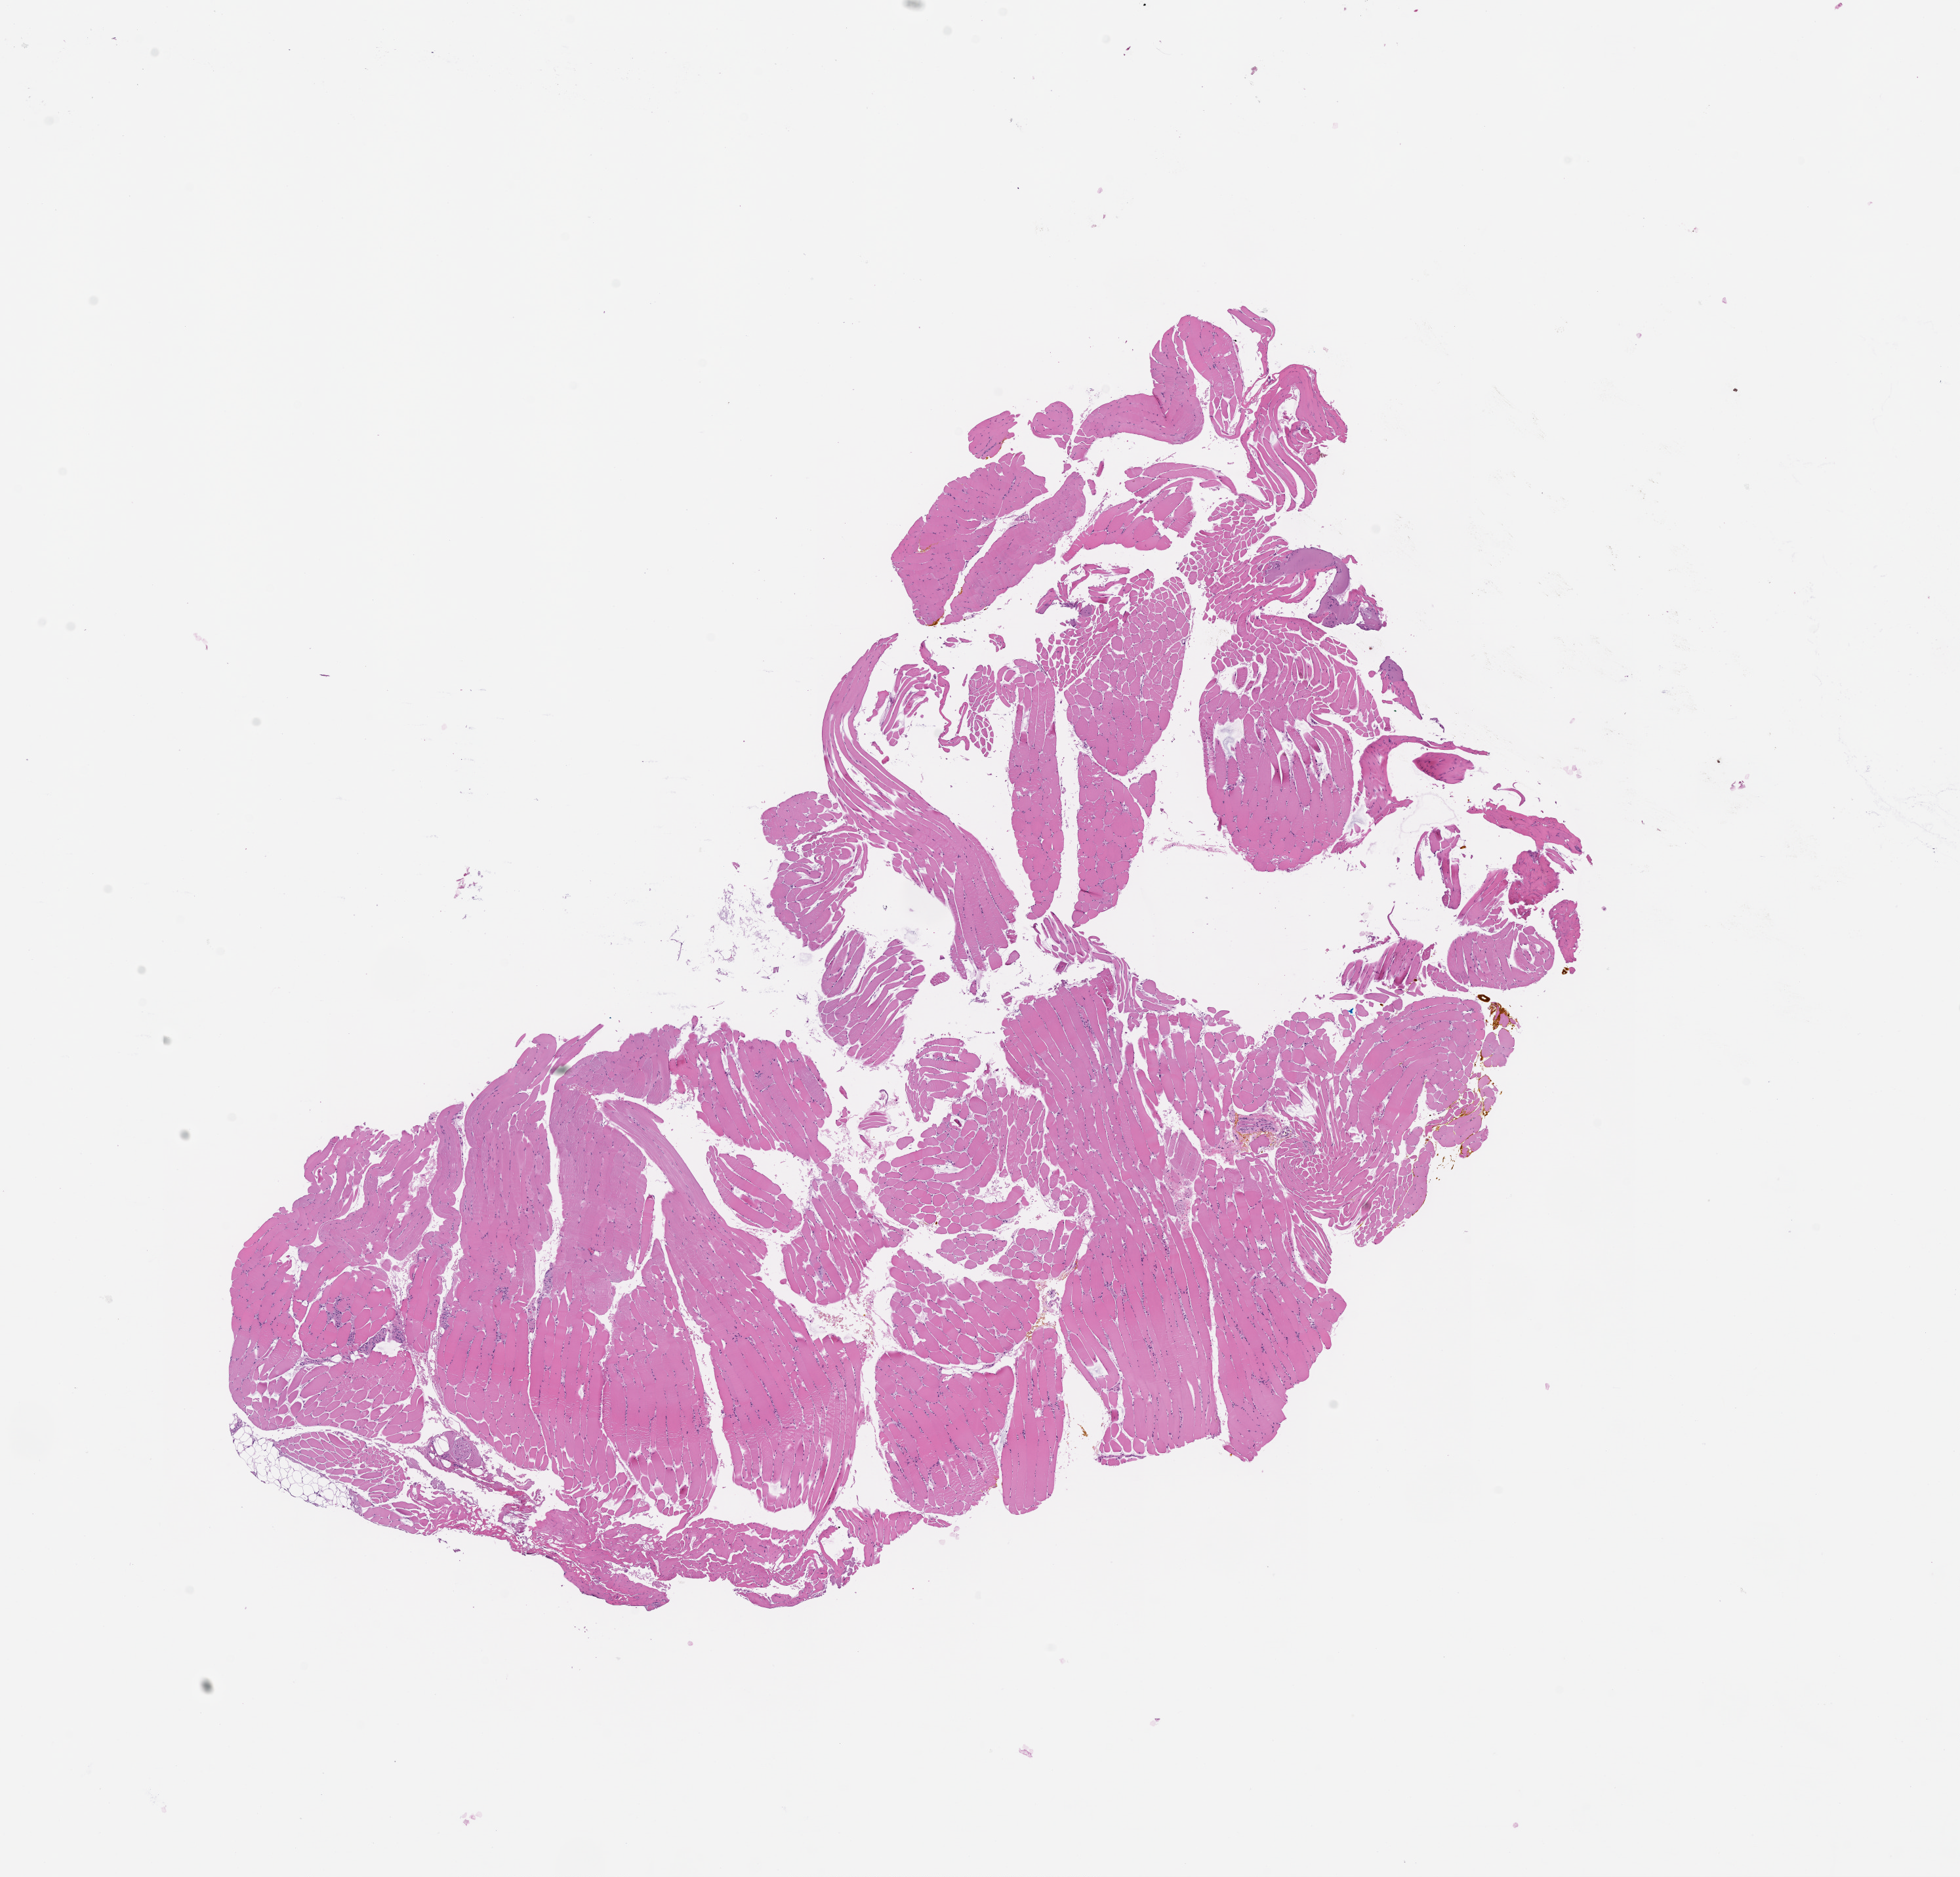
H&E-stained whole-slide image — low-resolution overview of the scanned area, about 12.0 x 11.5 mm (slide scanned at 20x).
Patient diagnosis (cohort enrolment): sarcoma (site not recorded at cohort level).